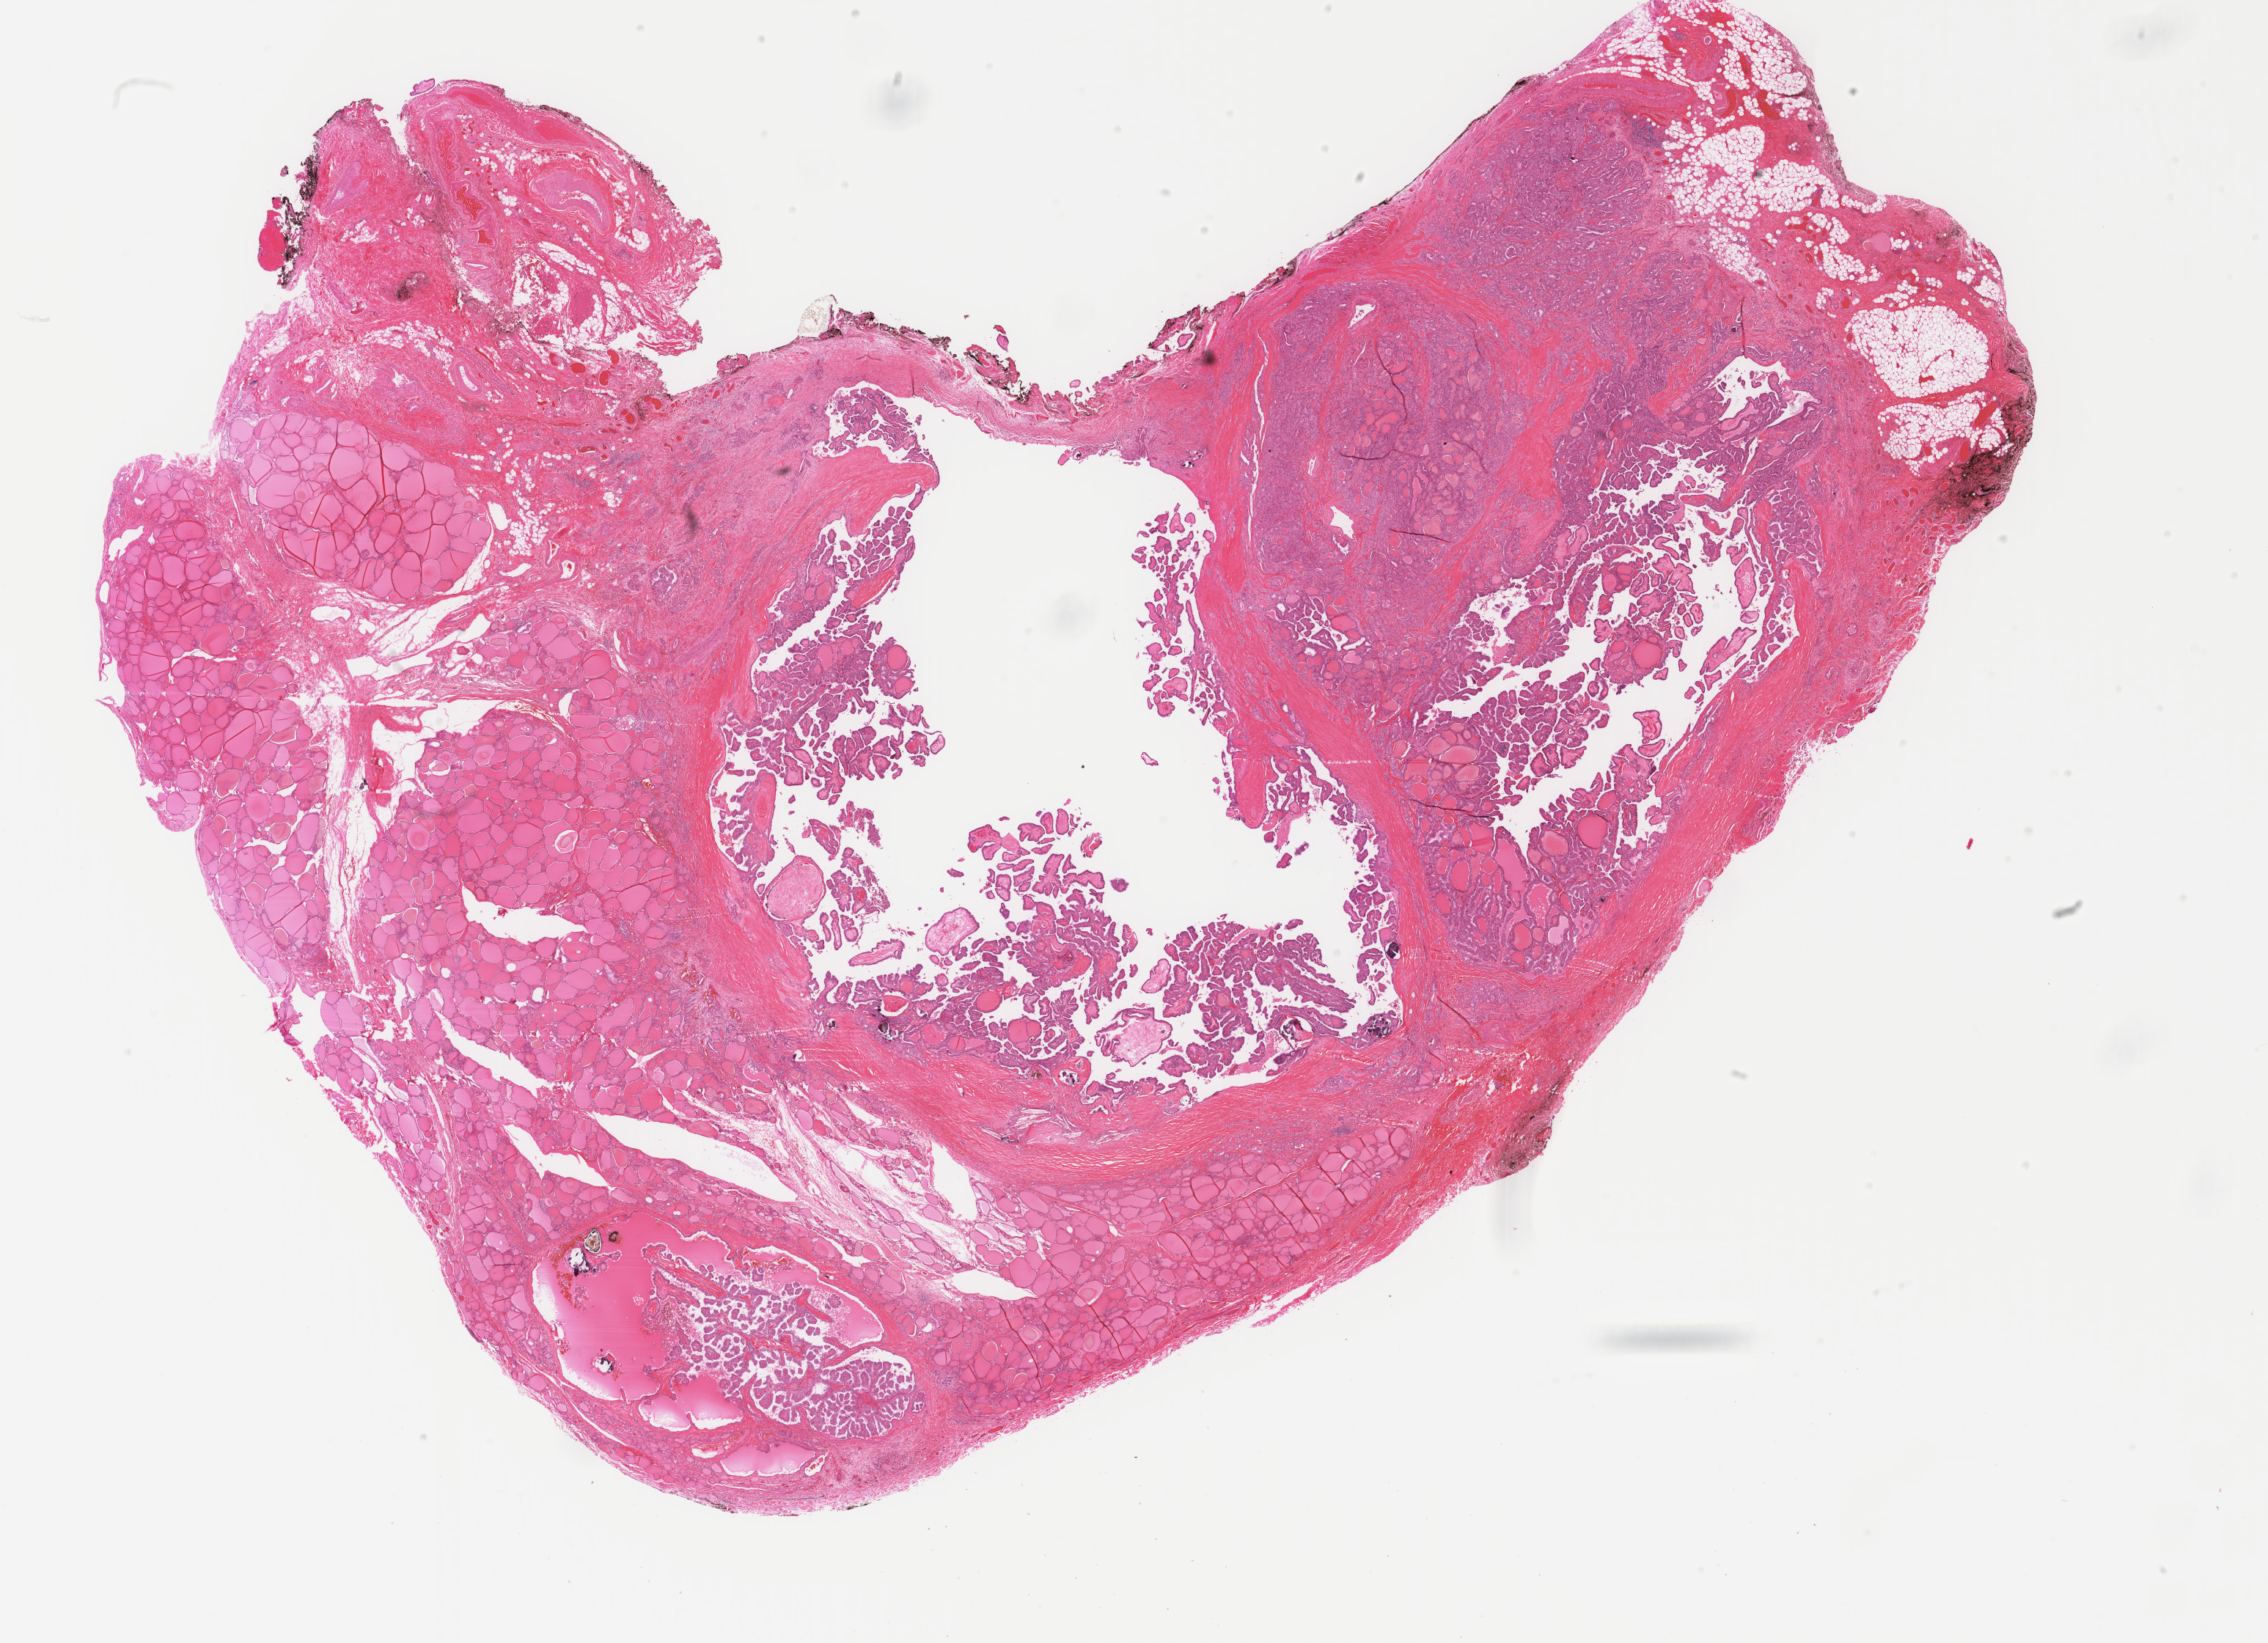
H&E whole-slide image, shown as a low-resolution overview of the whole scanned area (about 24.6 x 17.8 mm, slide scanned at 40x). Formalin-fixed paraffin-embedded (FFPE) diagnostic section. Thyroid, primary tumour sample. Female, age 35 years at initial diagnosis.
AJCC pathologic stage: I (5th edition). Diagnosis: Papillary adenocarcinoma, NOS (thyroid gland). Lymph nodes positive (case pathology): 14 of 44 examined.